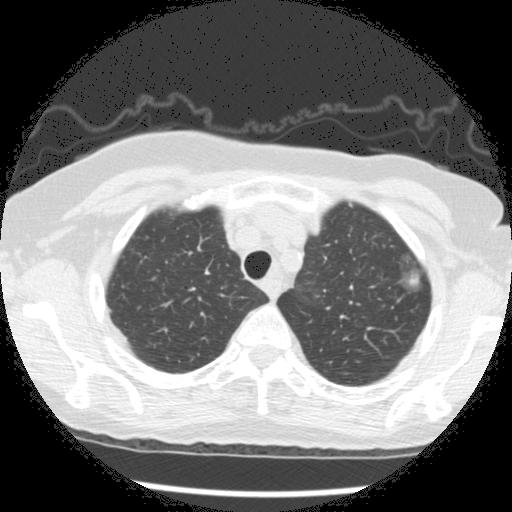
Chest CT (low-dose screening protocol), one axial image, second annual screen, lung window (W 1500 / L -600 HU), 2.5 mm slice thickness, slice 37 of 266 in the series. Female, age 73 years at enrolment.
Lesion marked by an expert reader, bounding box [x1, y1, x2, y2] px = [389, 248, 432, 292]. The screening reader recorded 3 non-calcified nodules or masses ≥4 mm on this exam (left upper lobe, left upper lobe, left upper lobe); which of them this box marks is not recorded. Official screen result: positive, change unspecified: nodule(s) >= 4 mm or enlarging nodule(s), mass(es), or other non-specific abnormalities suspicious for lung cancer. Later outcome: lung cancer diagnosed 49 days after this screen — bronchiolo-alveolar adenocarcinoma, NOS, left upper lobe, well differentiated (G1), stage IA (AJCC 6th edition), 10 mm at pathology.